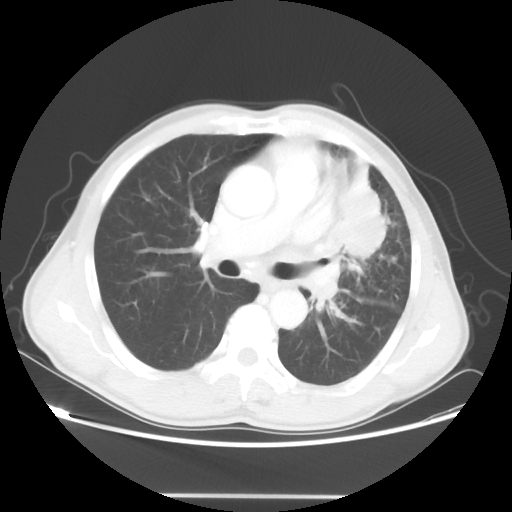
Chest CT, one axial slice. Slice 30 of 55 in the series (ordered by position). Lung window (W 1500 / L -600 HU). 5 mm slice thickness. 512 × 512 image matrix, field of view 398 × 398 mm. Patient: male, 60 years. From the clinical record (not read from this slice): clinical TNM (as recorded): T3 N3 M0.
Structures marked on this image (rectangle marked by the reading radiologist):
- lung tumour (recorded histology: adenocarcinoma): bounding box <339,165,387,266> (left, top, right, bottom; pixels)